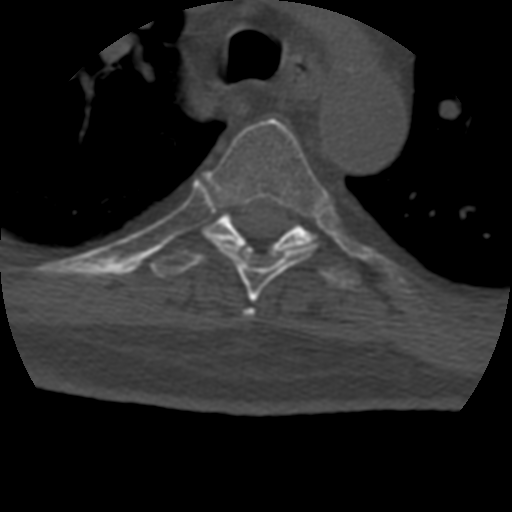
CT including the spine, one axial slice; slice 313 of 399 in the series (ordered by position); reconstruction kernel STANDARD; 120 kVp; bone window (W 1800 / L 400 HU); 1.25 mm slice thickness; 512 × 512 image matrix, field of view 160 × 160 mm. Patient age 69 years. From the clinical record (not read from this slice): primary cancer: prostate.
Annotated regions visible in this slice (semi-automatic segmentation, software-assisted and operator-edited):
- T4 vertebra: bounding box (x1, y1, x2, y2) in pixels: (244, 308, 255, 316)
- T5 vertebra: (204, 118, 329, 303)
- T6 vertebra: (150, 212, 360, 288)